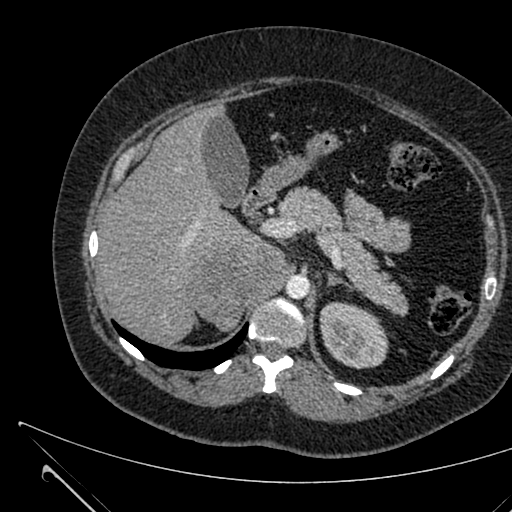
Contrast-enhanced abdominal CT, one axial slice; intravenous contrast given; soft-tissue window (W 400 / L 40 HU); 1 mm slice thickness; 512 × 512 image matrix, field of view 376 × 376 mm. Female patient, age 36 years. Case-level facts recorded for this patient, not image findings: diagnosis: adrenocortical carcinoma; tumour side: right adrenal; tumour size at pathology: 10 cm; Ki-67 index: 20 %; stage (as recorded): 4.
Outlined on this slice (semi-automatically segmented with operator editing):
- mass: bounding box <192,245,292,332> (left, top, right, bottom; pixels)